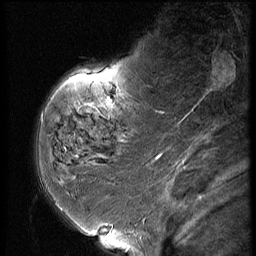
Breast MRI (dynamic contrast-enhanced), one sagittal slice. Position 14 of 56 along the scan axis. Dynamic contrast-enhanced series, image 2 of 3 at this slice position (ordered by acquisition). 1.5 T. TE 4.2 ms, TR 9 ms. 256 × 256 image matrix. Patient: female, 59 years. From the clinical record (not read from this slice): setting: breast cancer imaged before/during neoadjuvant chemotherapy; receptor status: HER2-positive.
Outlined on this slice (semi-automatic segmentation, software-assisted and operator-edited):
- analysis volume of interest (the breast-tissue region the enhancement analysis was run in; not a lesion): bounding box (x1, y1, x2, y2) in pixels: (44, 66, 151, 135)
- tumour enhancement mask (voxels above the 140 % enhancement threshold inside the analysis volume of interest): (107, 97, 112, 104)